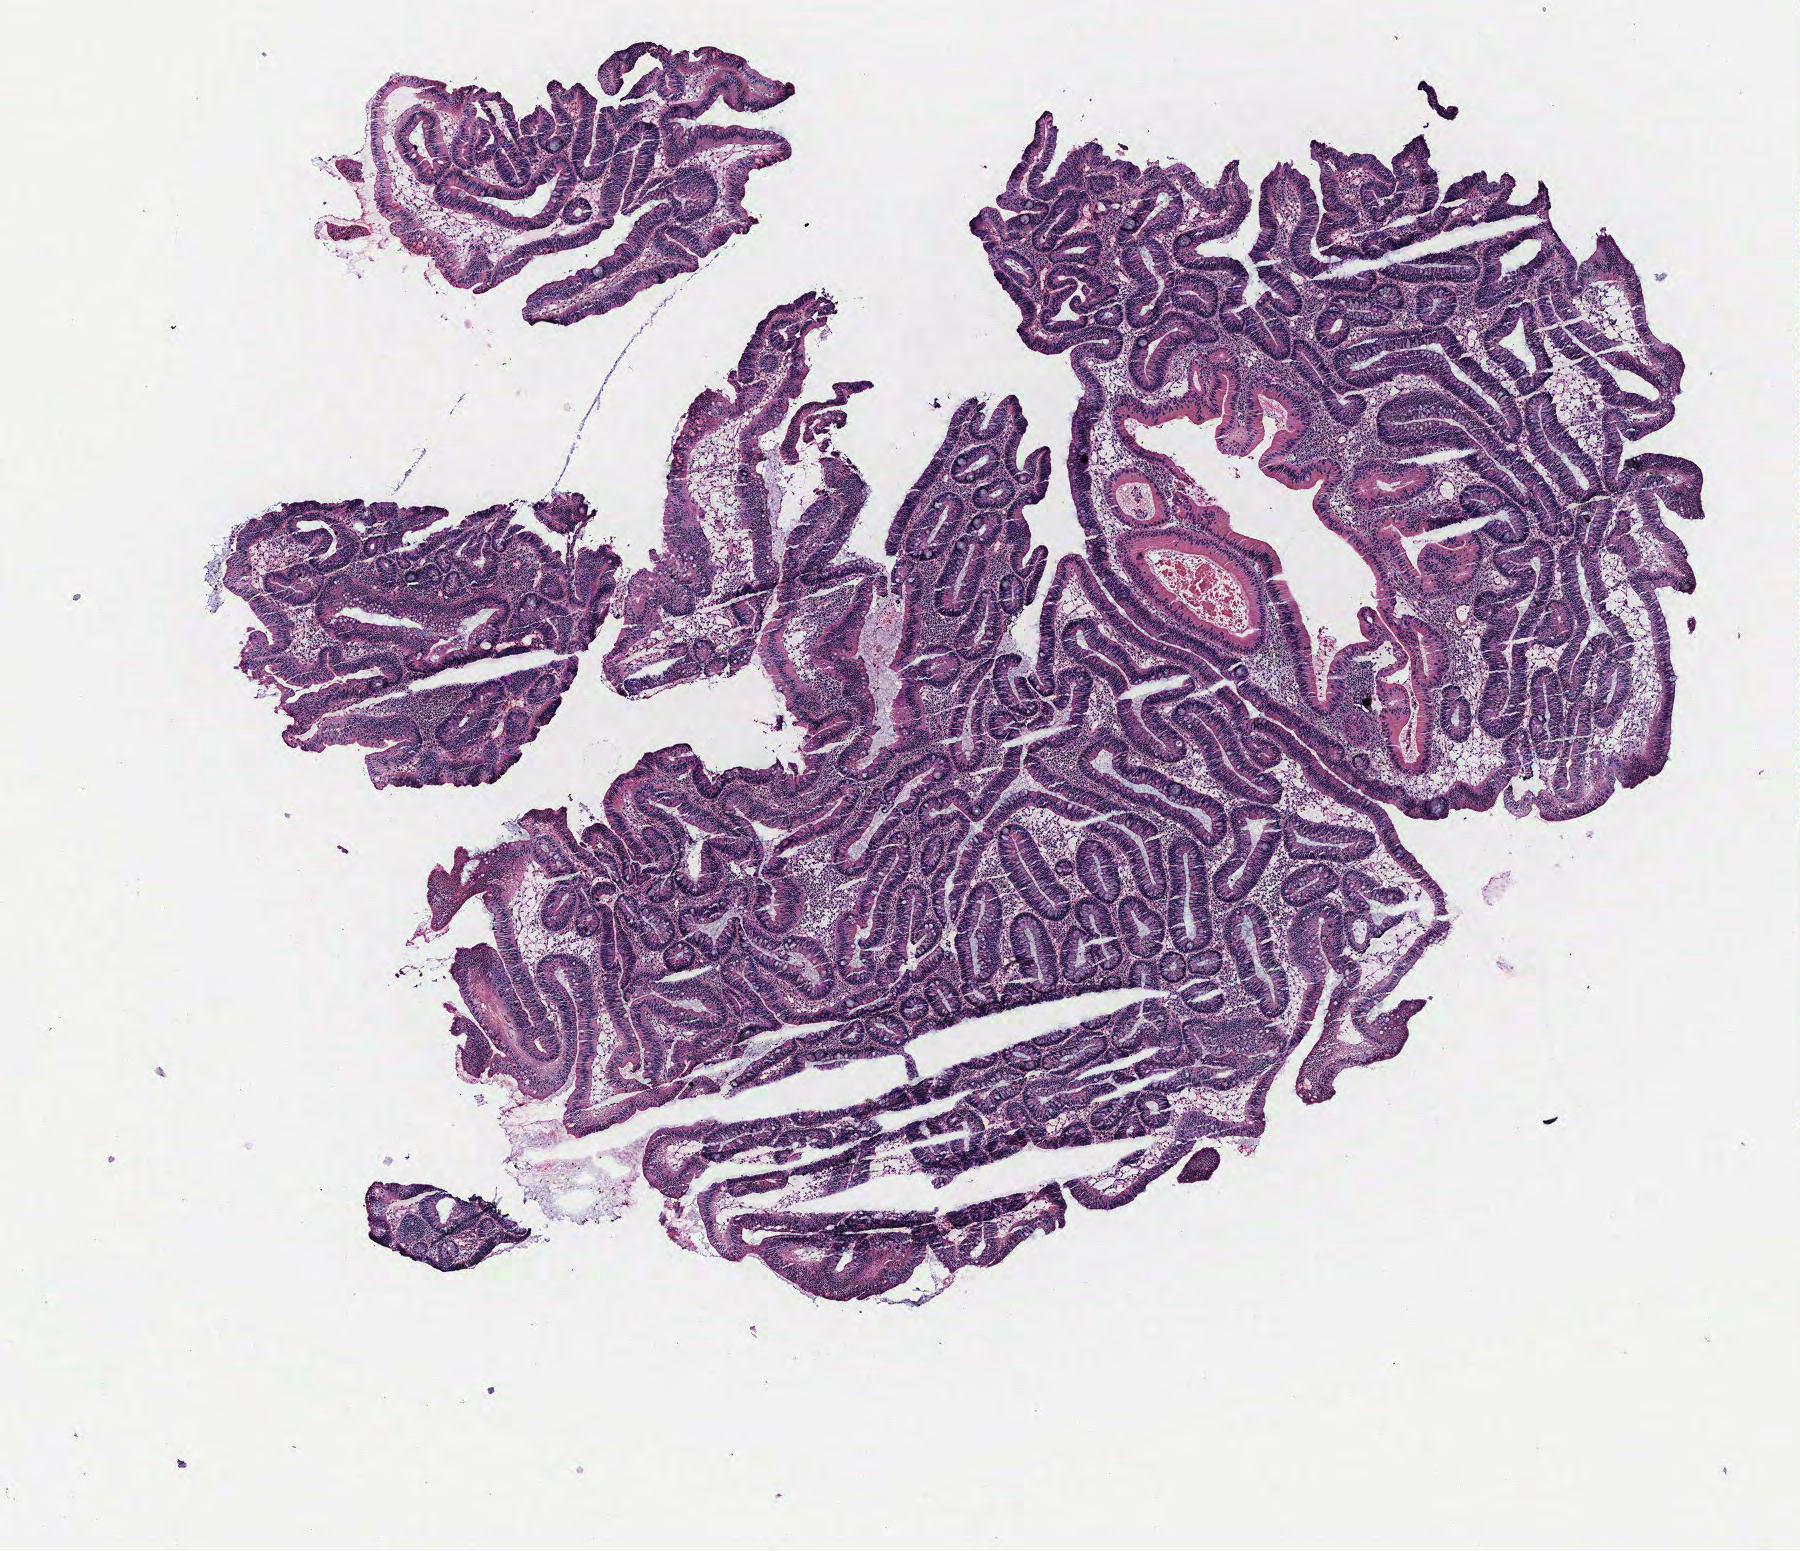
Whole-slide histology image, H&E — whole scanned area (about 7.2 x 6.2 mm) shown as a low-resolution overview, colon, tissue type not recorded.
Patient diagnosis (cohort enrolment): colon cancer (colon).